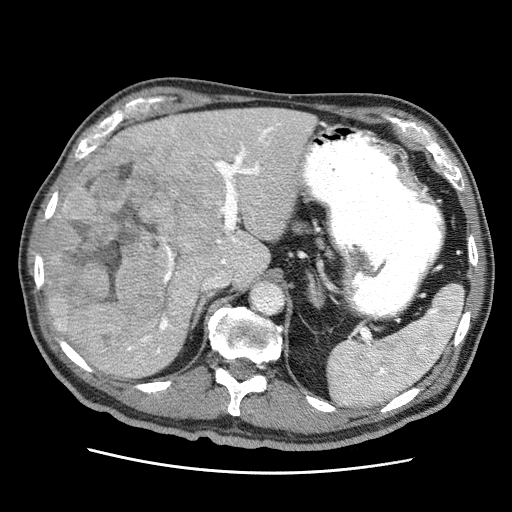
Contrast-enhanced abdominal CT (liver protocol), one axial slice; slice 35 of 75 in the series (ordered by position); 120 kVp; soft-tissue window (W 400 / L 40 HU); 2.5 mm slice thickness; 512 × 512 image matrix, field of view 360 × 360 mm. From the clinical record (not read from this slice): diagnosis: hepatocellular carcinoma (patient treated with transarterial chemoembolisation; whether this scan precedes or follows treatment is not stated here); TNM stage (as recorded): Stage-IIIA; Child-Pugh class: A; tumour differentiation: well differentiated; tumour nodularity: multinodular.
Outlined on this slice (semi-automatic segmentation, software-assisted and operator-edited):
- liver parenchyma outside the tumour (the mass and vessels are separate outlines, so this box may not span the whole liver): bounding box <46,108,316,378> (left, top, right, bottom; pixels)
- mass: <48,135,224,368>
- liver vessels: <58,117,280,354>